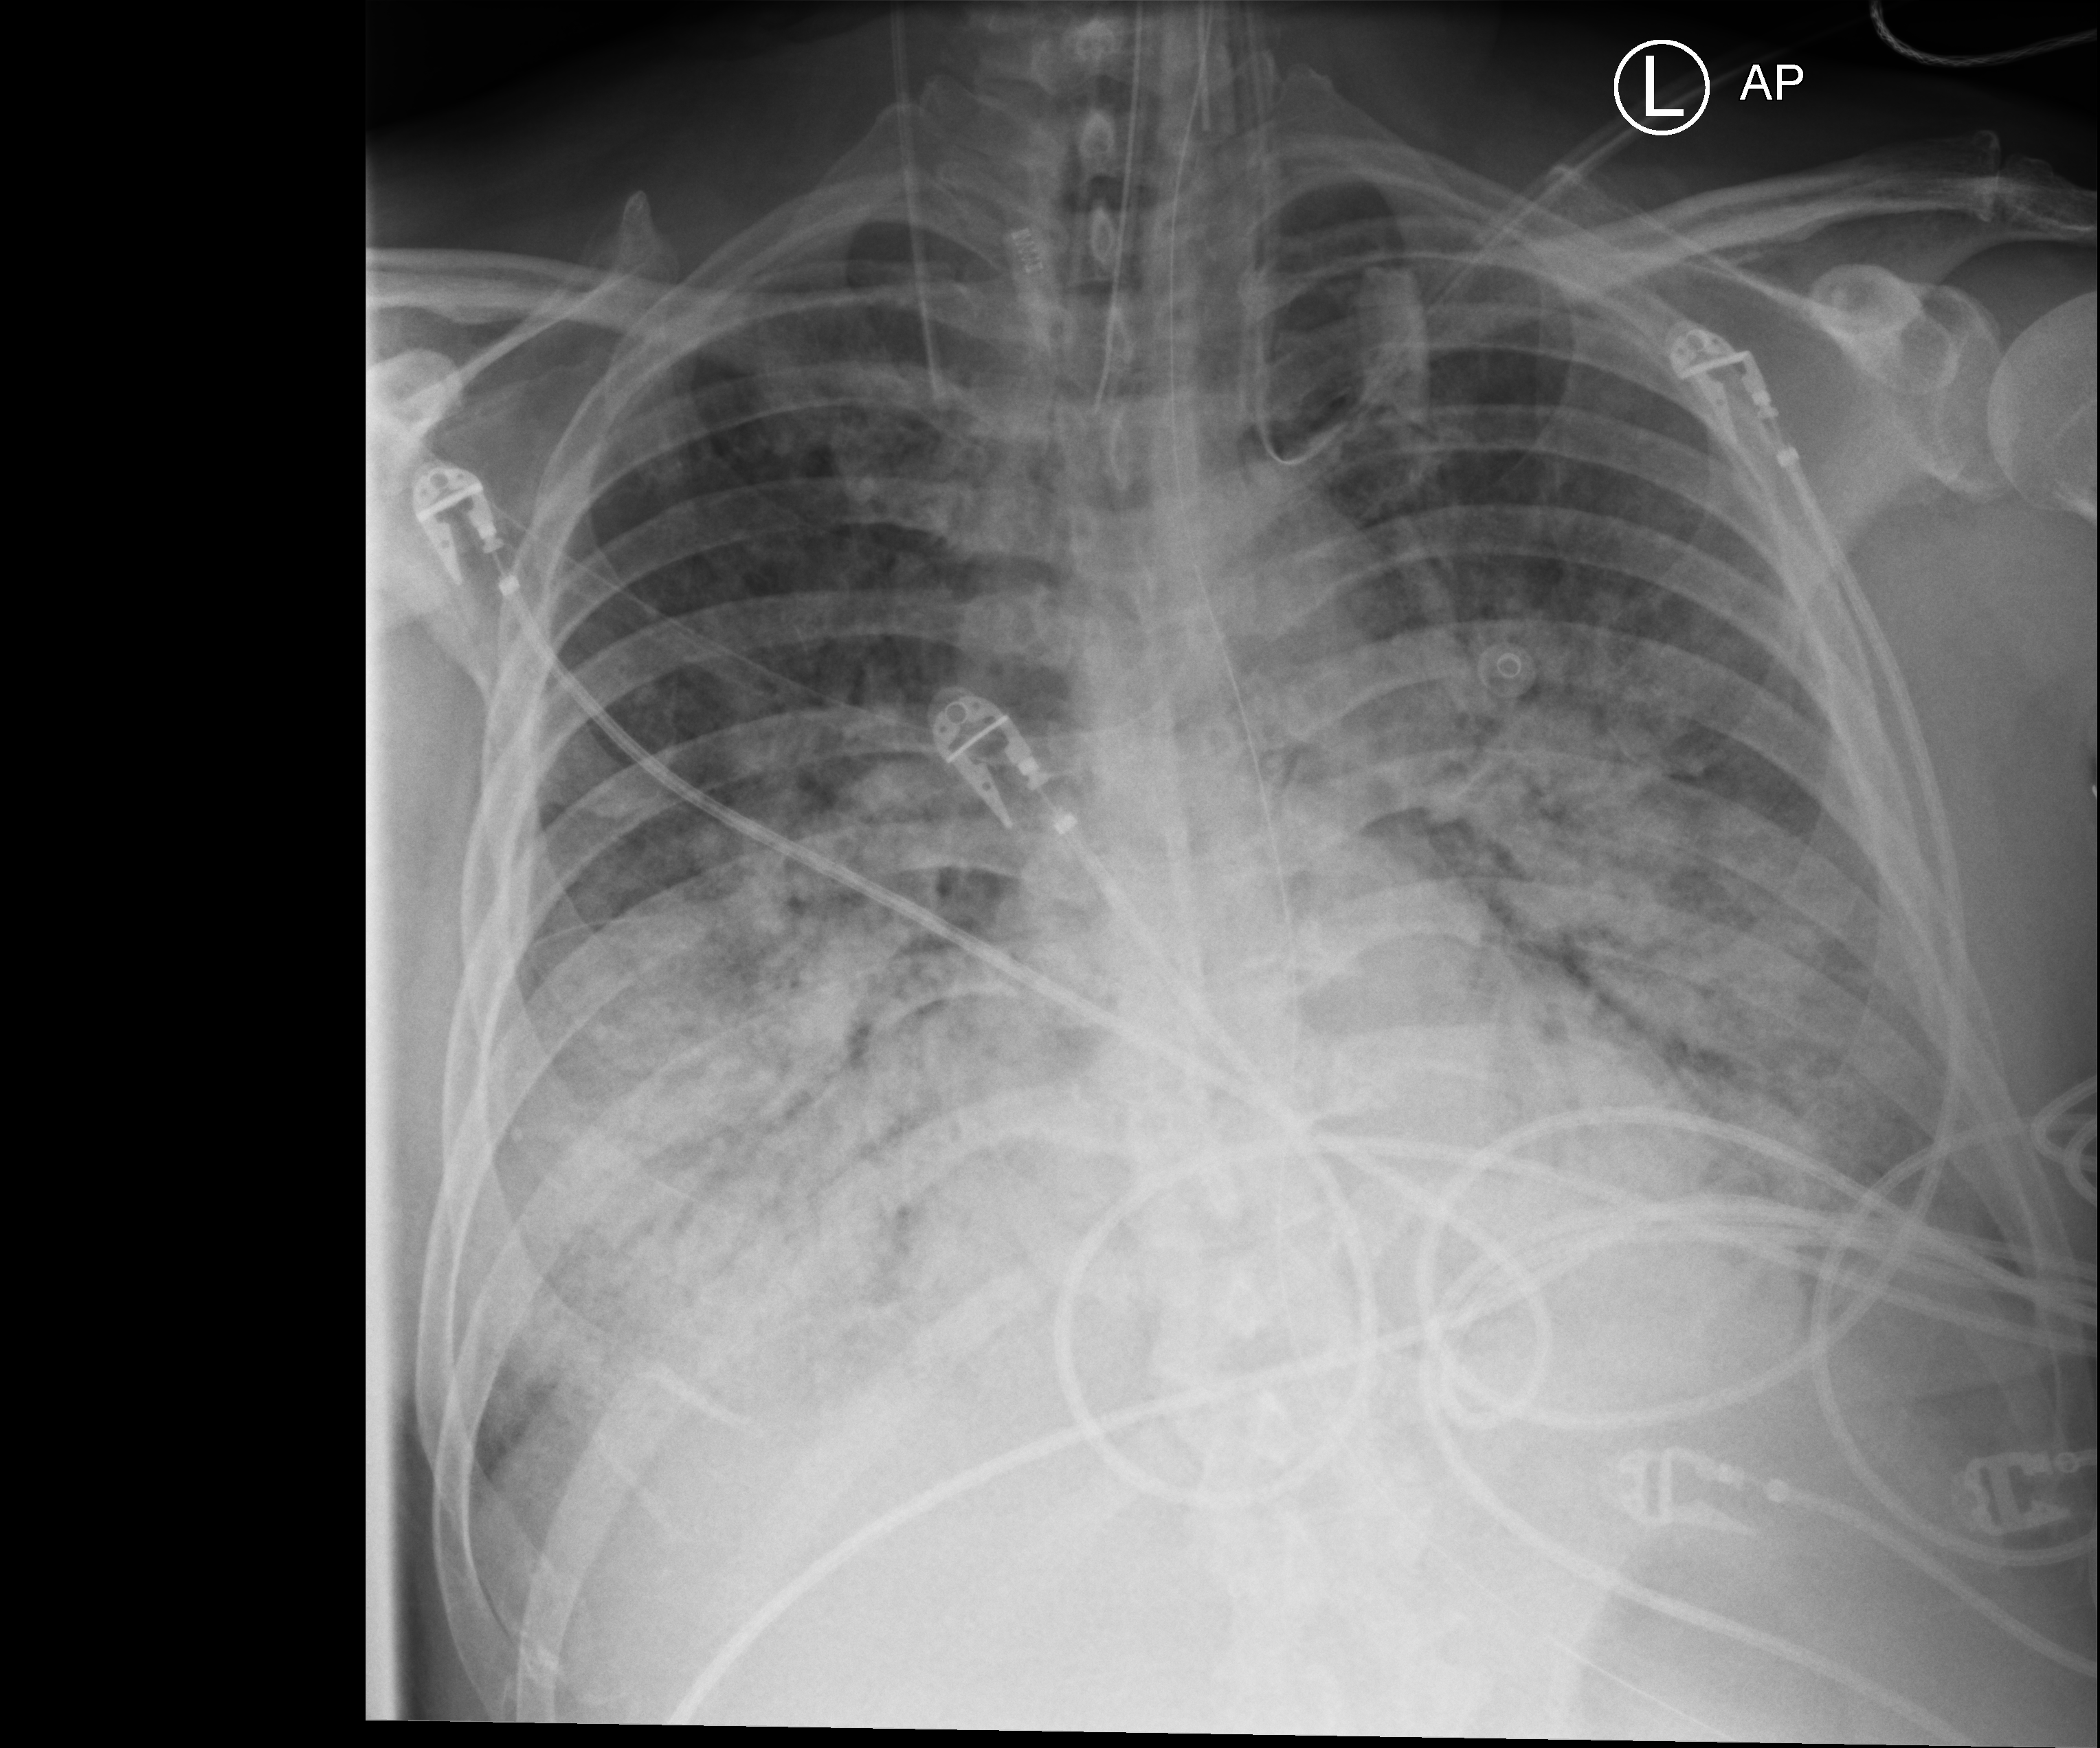
Bedside chest radiograph (computed radiography). Patient hospitalised with COVID-19; male, aged 60–74 years.
Admission-level facts for this patient (not findings on this image; timing relative to this image not recorded): mechanically ventilated during this hospital stay: yes.